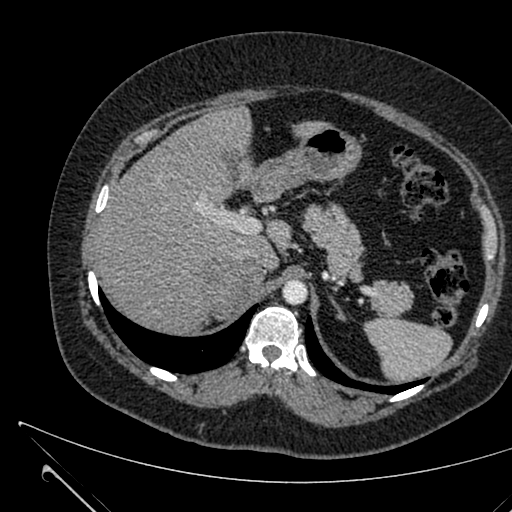
Contrast-enhanced abdominal CT, one axial slice; slice 472 of 731 in the series (ordered by position); 120 kVp; intravenous contrast given; soft-tissue window (W 400 / L 40 HU); 512 × 512 image matrix, field of view 376 × 376 mm. Patient: female, 36 years. Case-level facts recorded for this patient, not image findings: diagnosis: adrenocortical carcinoma; tumour side: right adrenal; tumour size at pathology: 10 cm; Ki-67 index: 20 %.
Structures marked on this image (semi-automatic segmentation, software-assisted and operator-edited):
- mass: bounding box <205,262,263,316> (left, top, right, bottom; pixels)